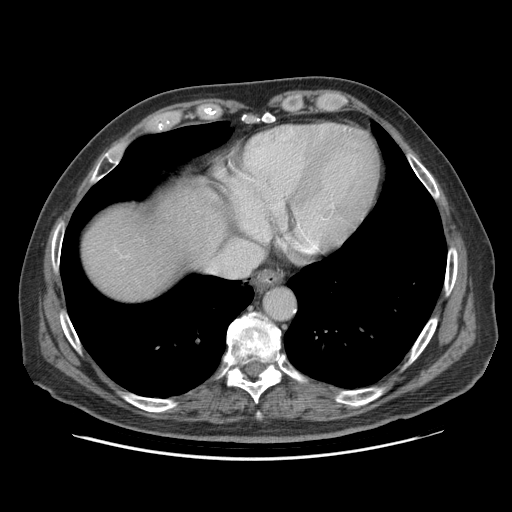
Contrast-enhanced abdominal CT (liver protocol), one axial slice. Position 81 of 95 along the scan axis. 140 kVp. Soft-tissue window (W 400 / L 40 HU). 512 × 512 image matrix, field of view 400 × 400 mm. From the clinical record (not read from this slice): diagnosis: hepatocellular carcinoma (patient treated with transarterial chemoembolisation; whether this scan precedes or follows treatment is not stated here); TNM stage (as recorded): Stage-IVB; Child-Pugh class: A.
Structures marked on this image (semi-automatic segmentation, software-assisted and operator-edited):
- liver parenchyma outside the tumour (the mass and vessels are separate outlines, so this box may not span the whole liver): bounding box (x1, y1, x2, y2) in pixels: (82, 180, 226, 300)